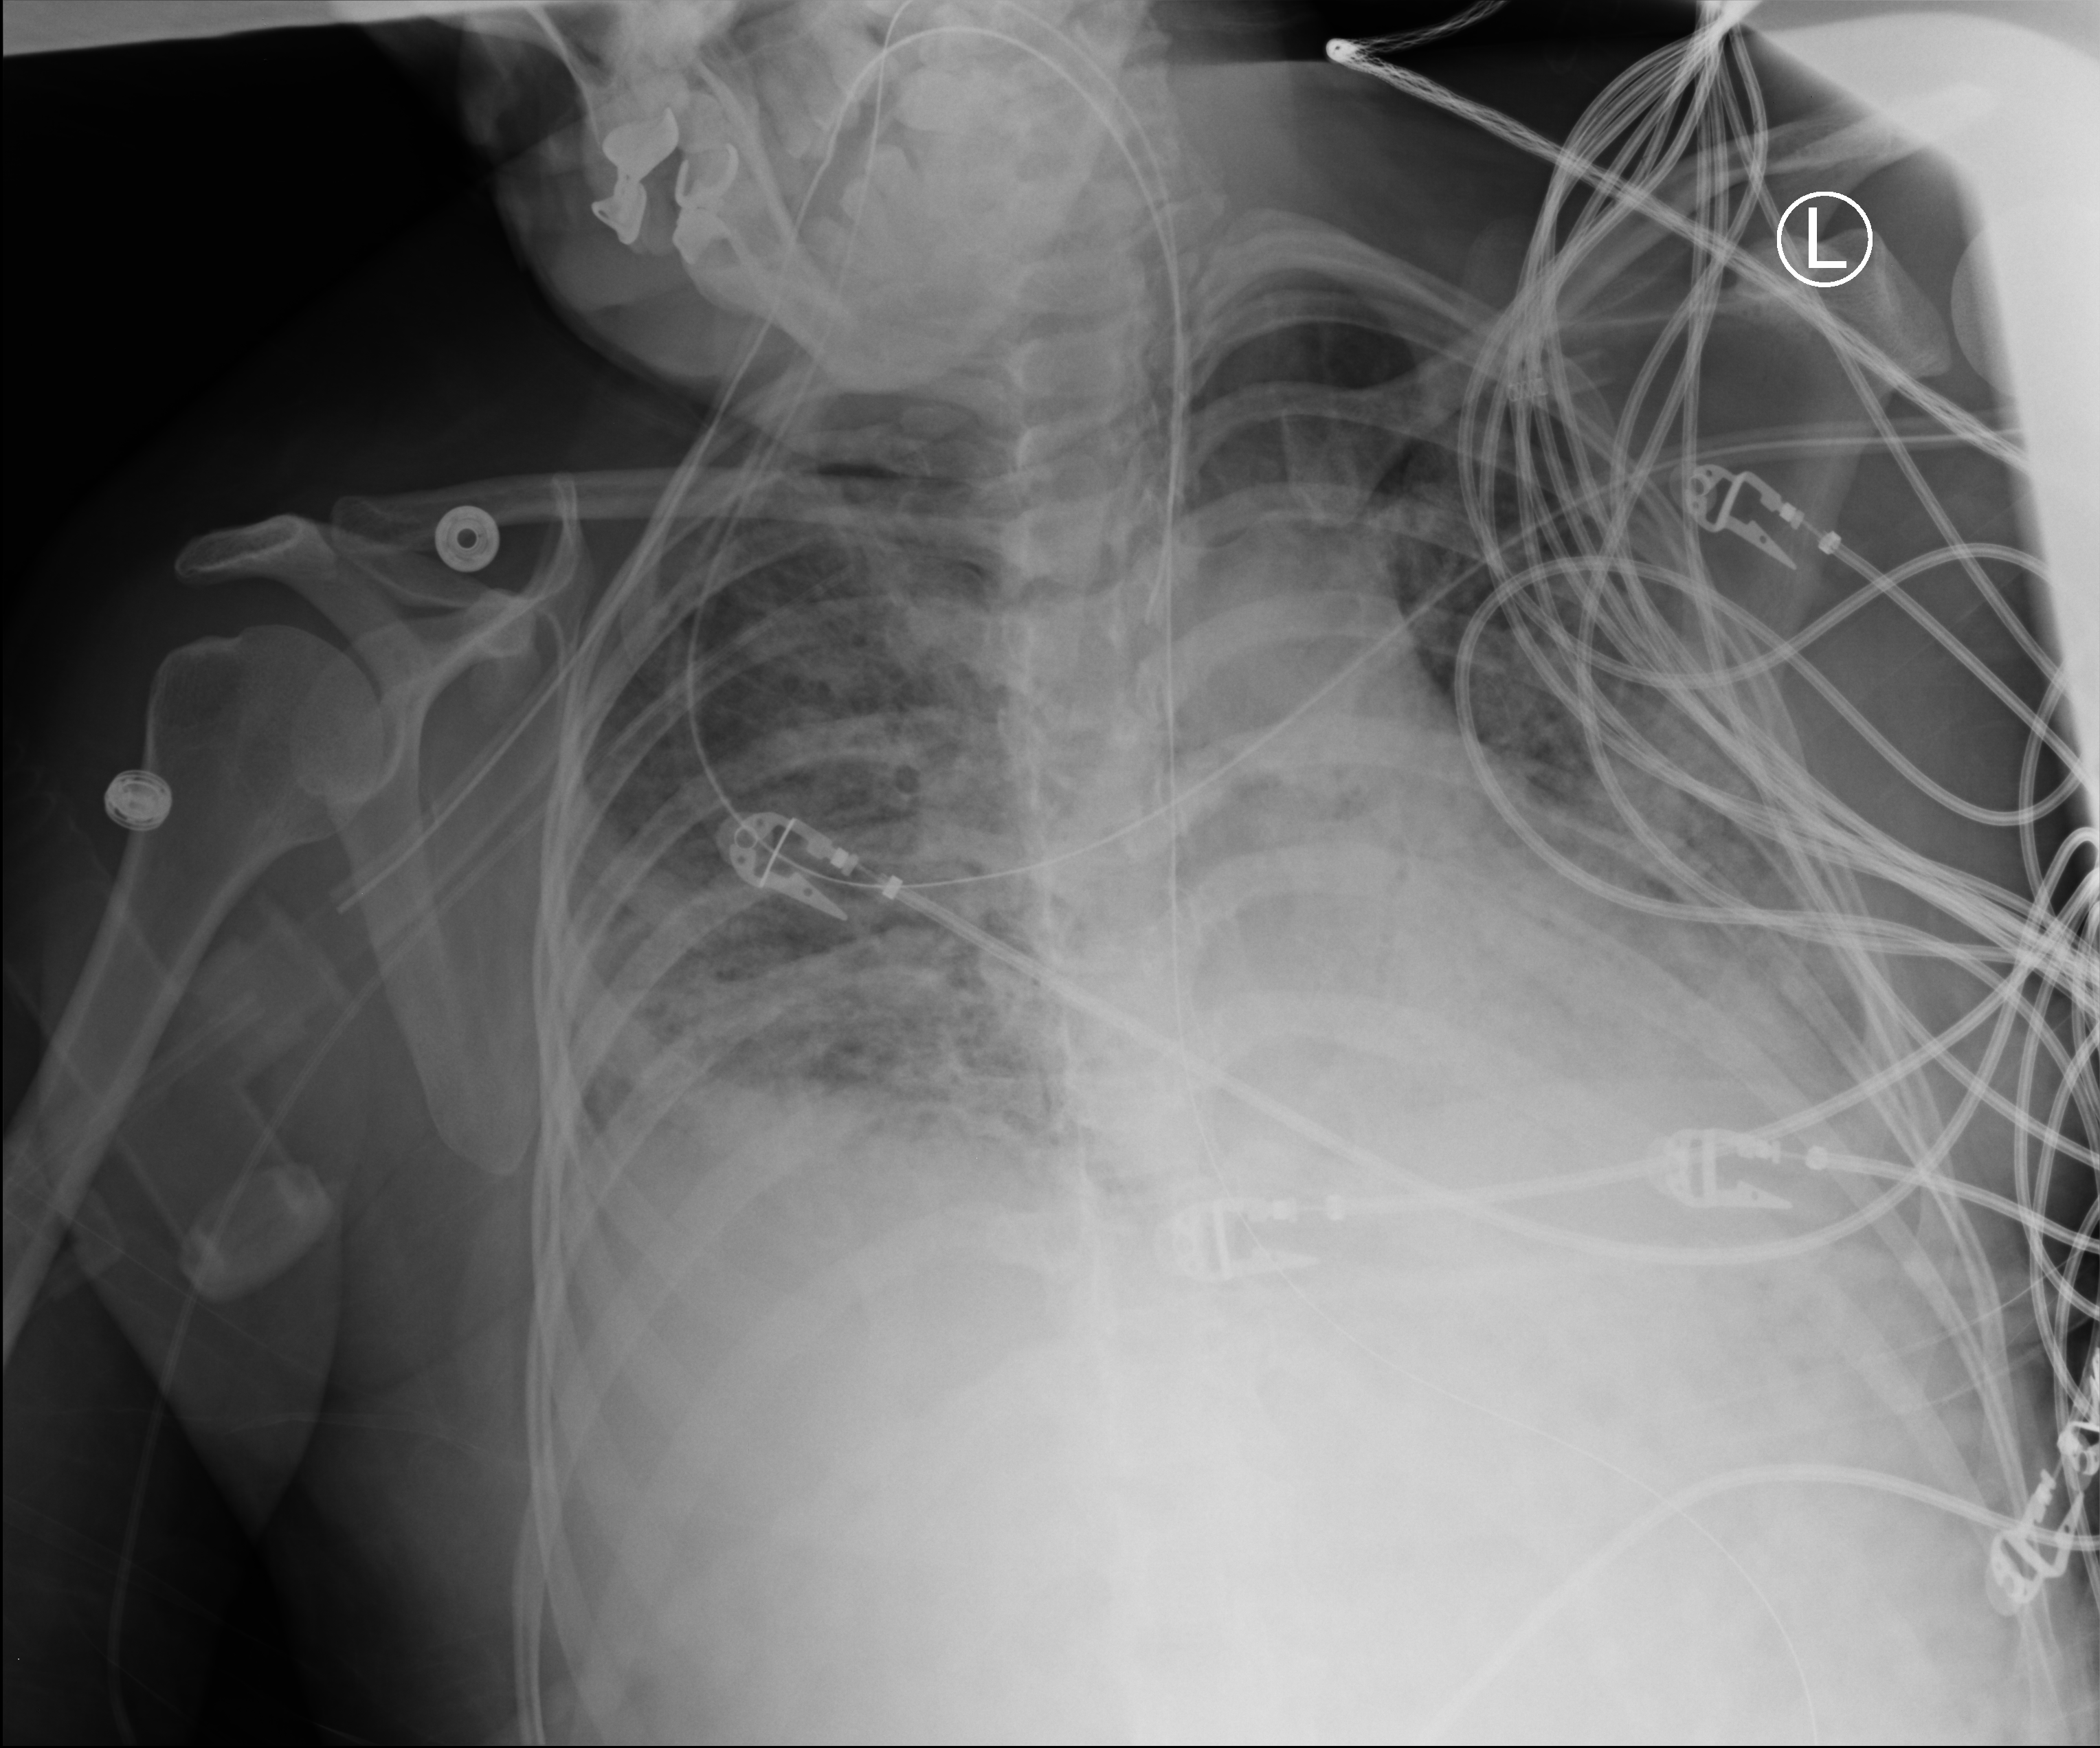
Bedside chest radiograph (computed radiography). Patient hospitalised with COVID-19; female, aged 18–59 years.
Hospital-stay facts (about this admission, not read from this image; timing relative to this image not recorded):
- hypertension (admission record): no